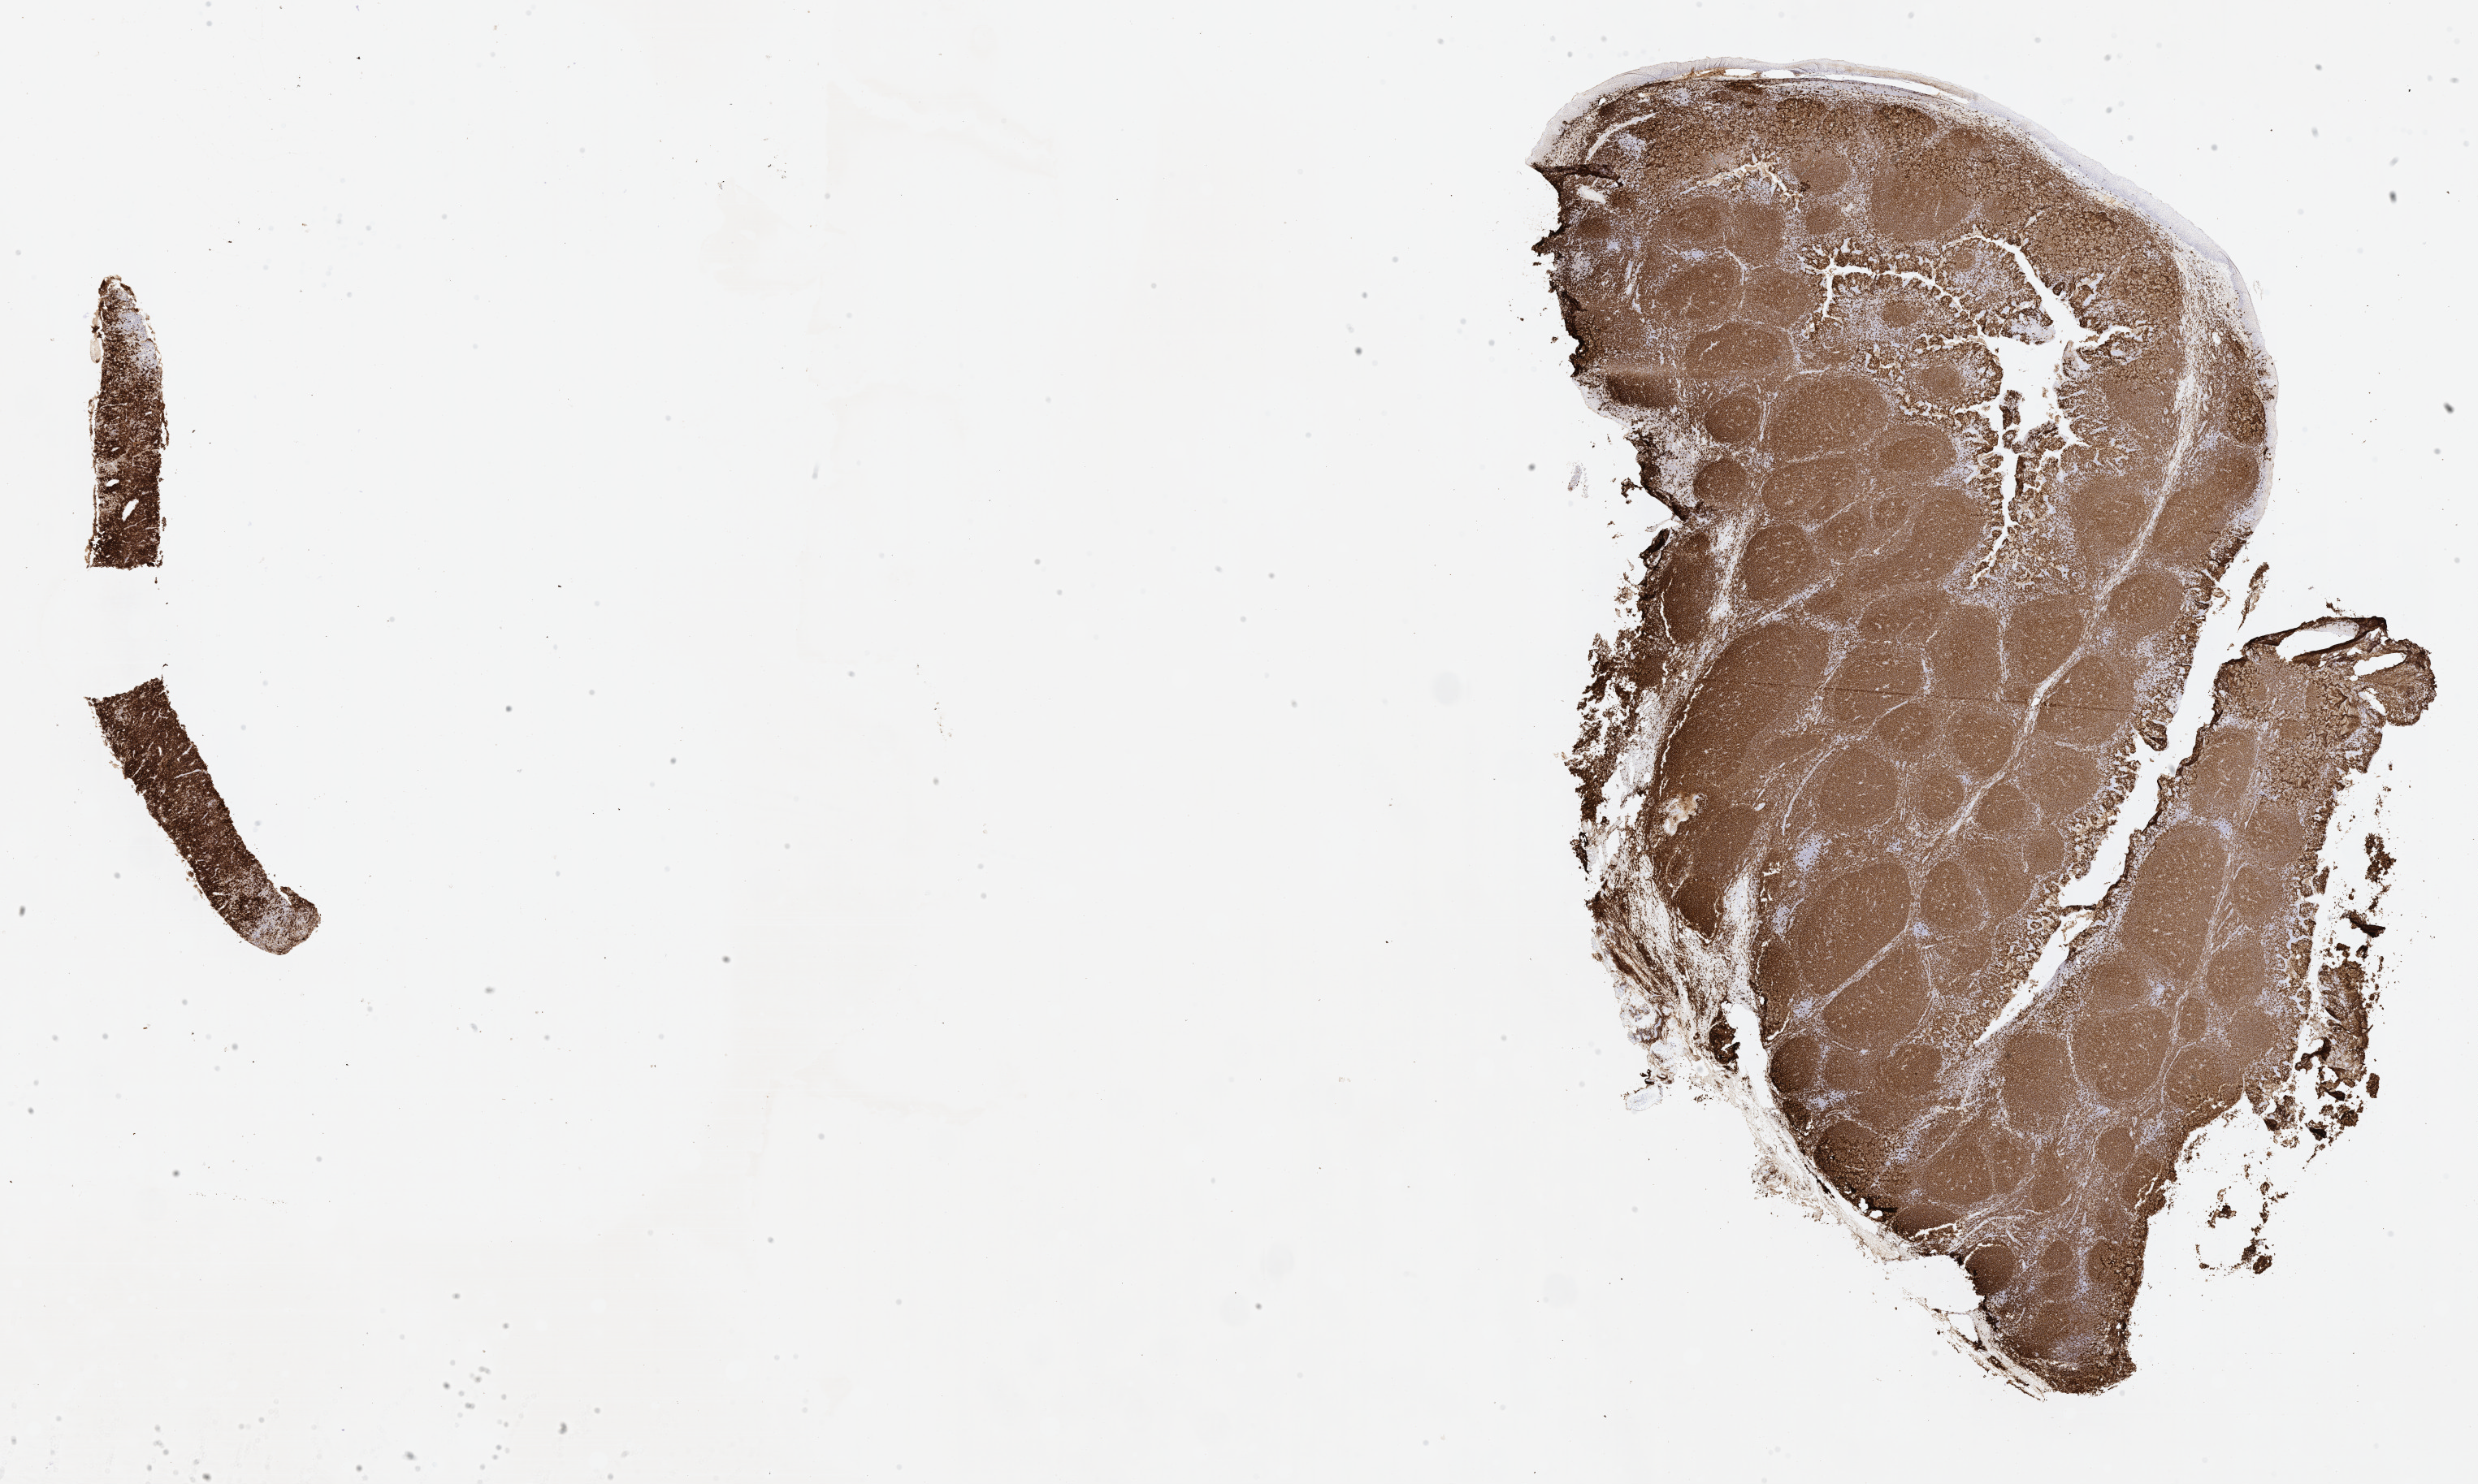
Immunohistochemistry (IHC) whole-slide image stained for CD20, low-resolution overview of the scanned area, about 24.7 x 14.8 mm. Patient sex: male.
Specimen: tumor tissue.